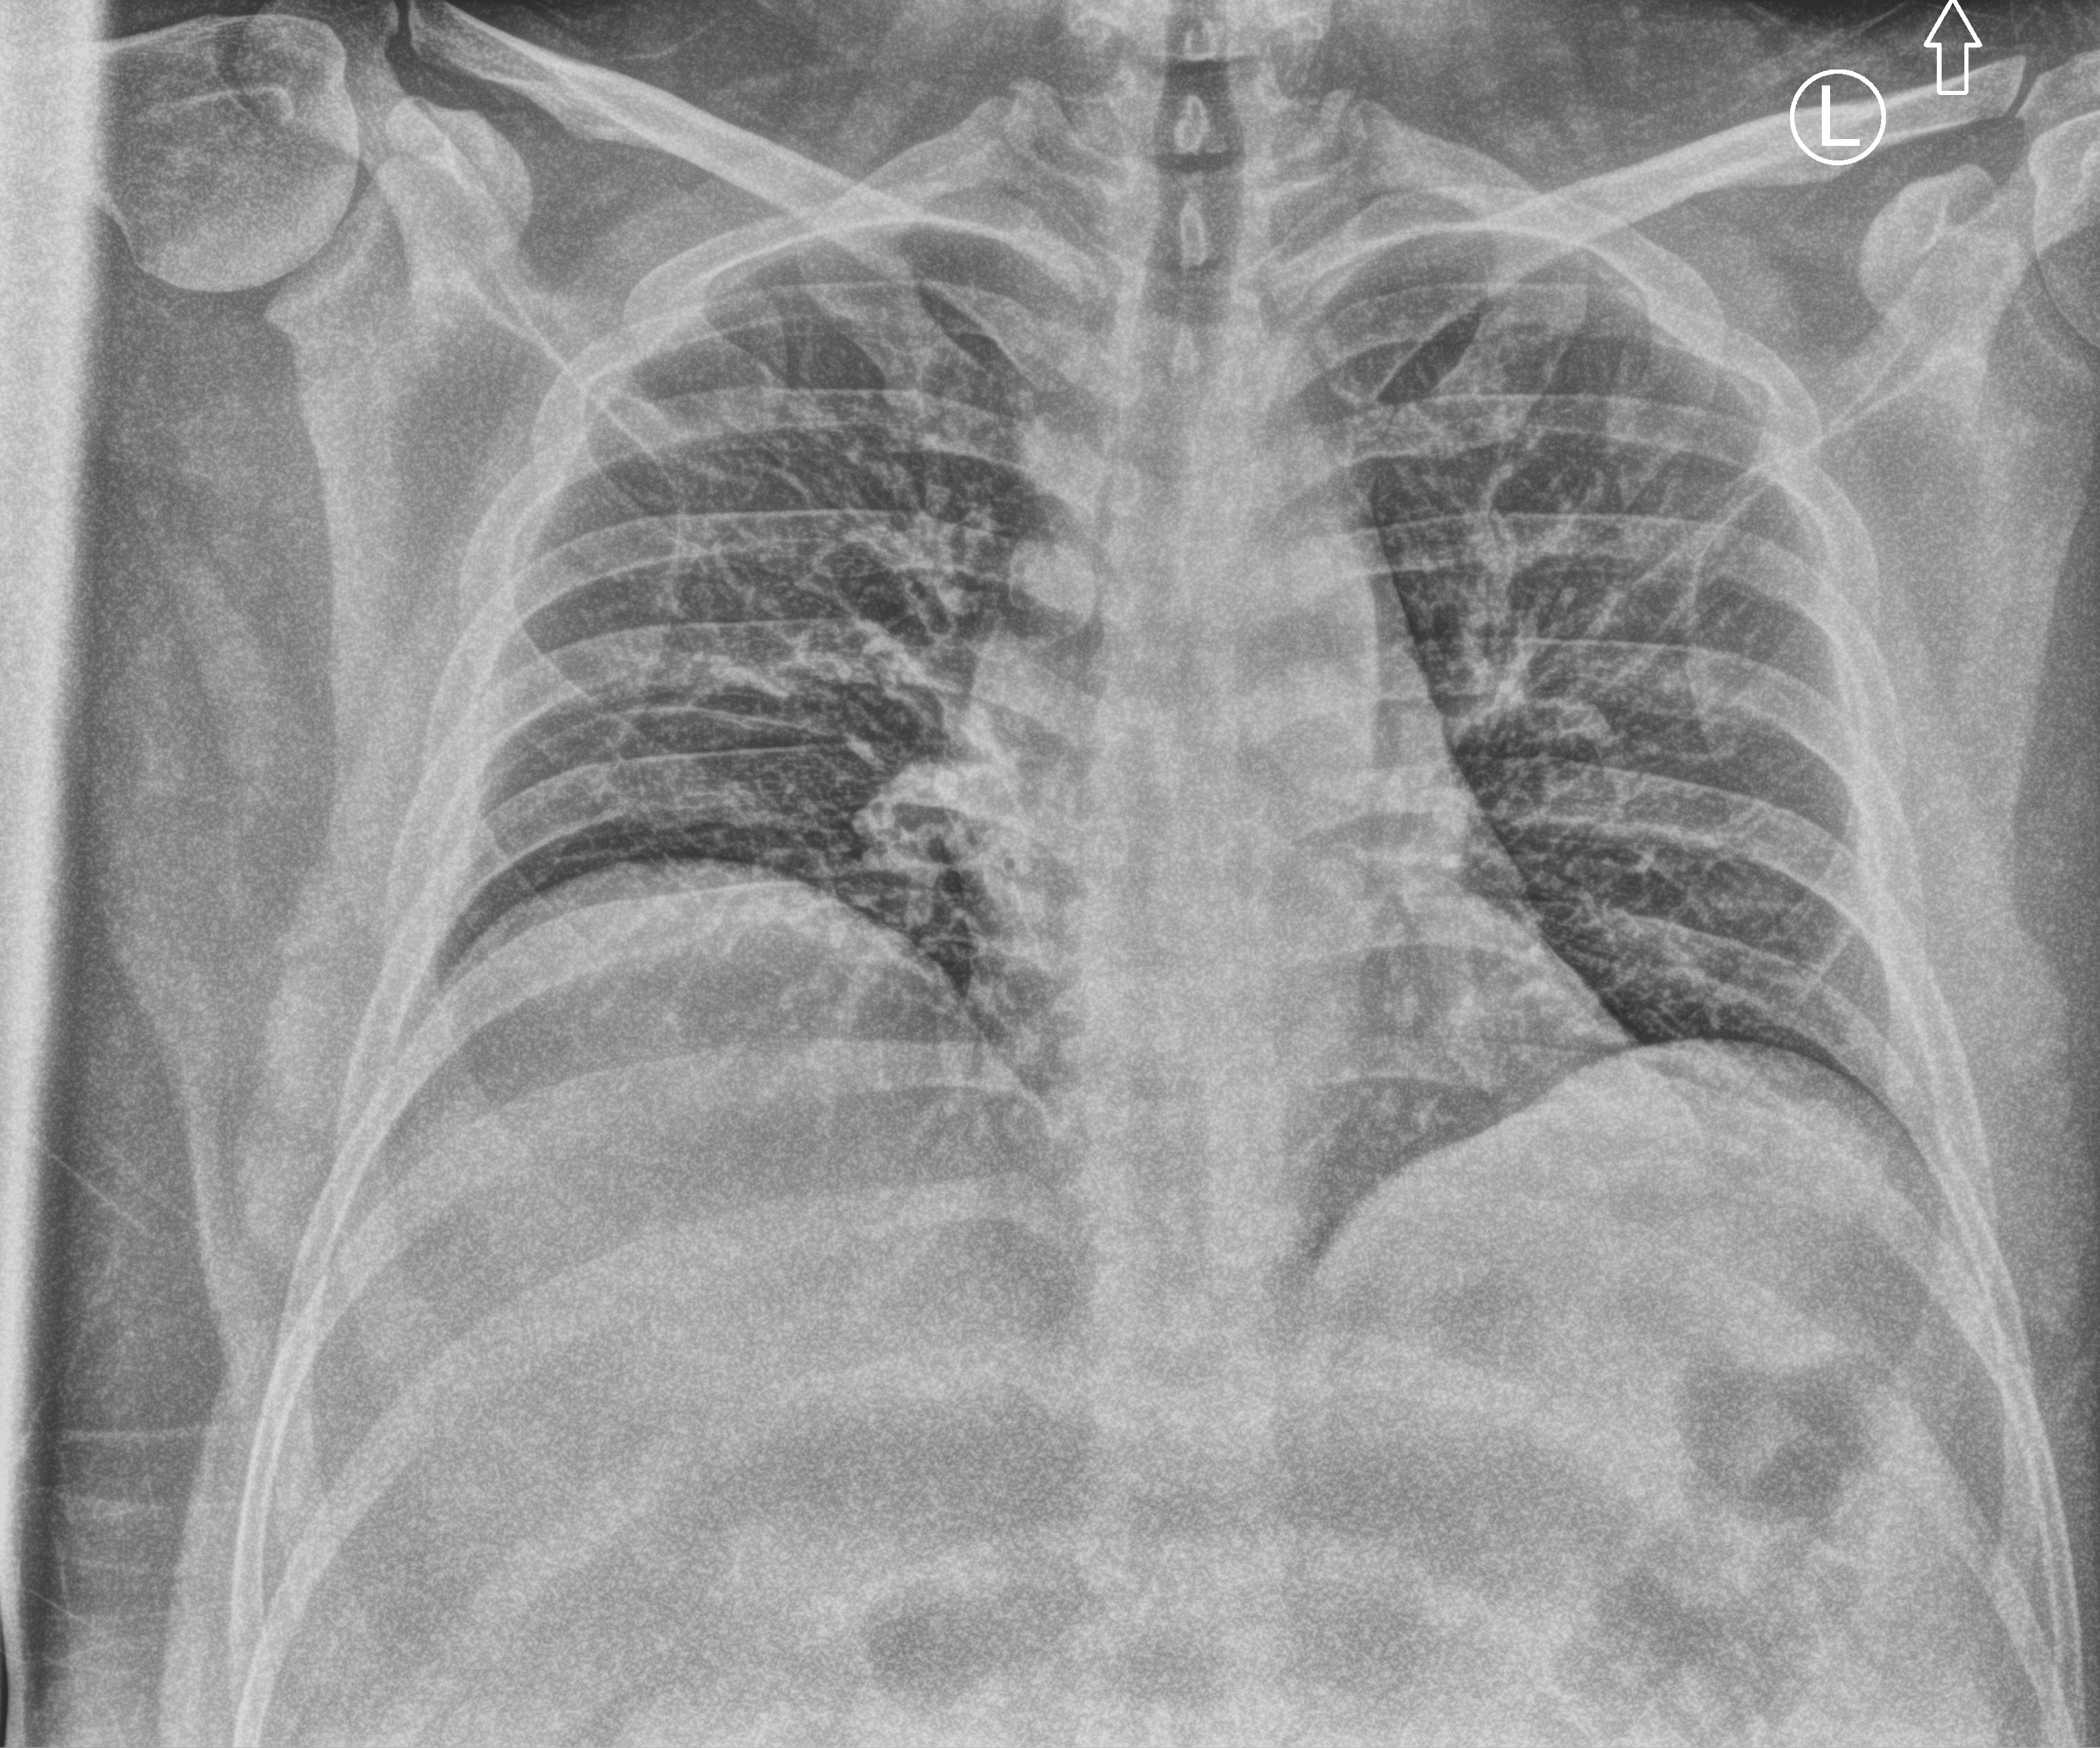
Portable chest radiograph; anteroposterior (AP) projection. Male patient hospitalised with COVID-19, age 18–59 years.
Hospital-stay facts (about this admission, not read from this image; timing relative to this image not recorded):
- admitted to intensive care during this hospital stay: no
- mechanically ventilated during this hospital stay: no